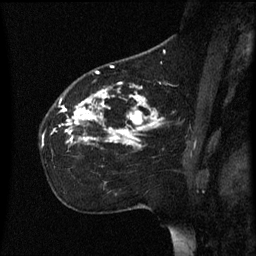
Breast MRI (dynamic contrast-enhanced), one sagittal slice. Slice 38 of 60 in the series (ordered by position). Dynamic contrast-enhanced series, image 2 of 3 at this slice position (ordered by acquisition). 1.5 T. TE 4.2 ms, TR 8.4 ms. 256 × 256 image matrix, field of view 200 × 200 mm. Patient: female, 35 years. Case-level facts recorded for this patient, not image findings: setting: breast cancer imaged before/during neoadjuvant chemotherapy; receptor status: HER2-positive.
Outlined on this slice (semi-automatically segmented with operator editing):
- analysis volume of interest (the breast-tissue region the enhancement analysis was run in; not a lesion): box from (x=42, y=78) to (x=165, y=159) px
- tumour enhancement mask (voxels above the 70 % enhancement threshold inside the analysis volume of interest): (x=61, y=82)–(x=163, y=147)